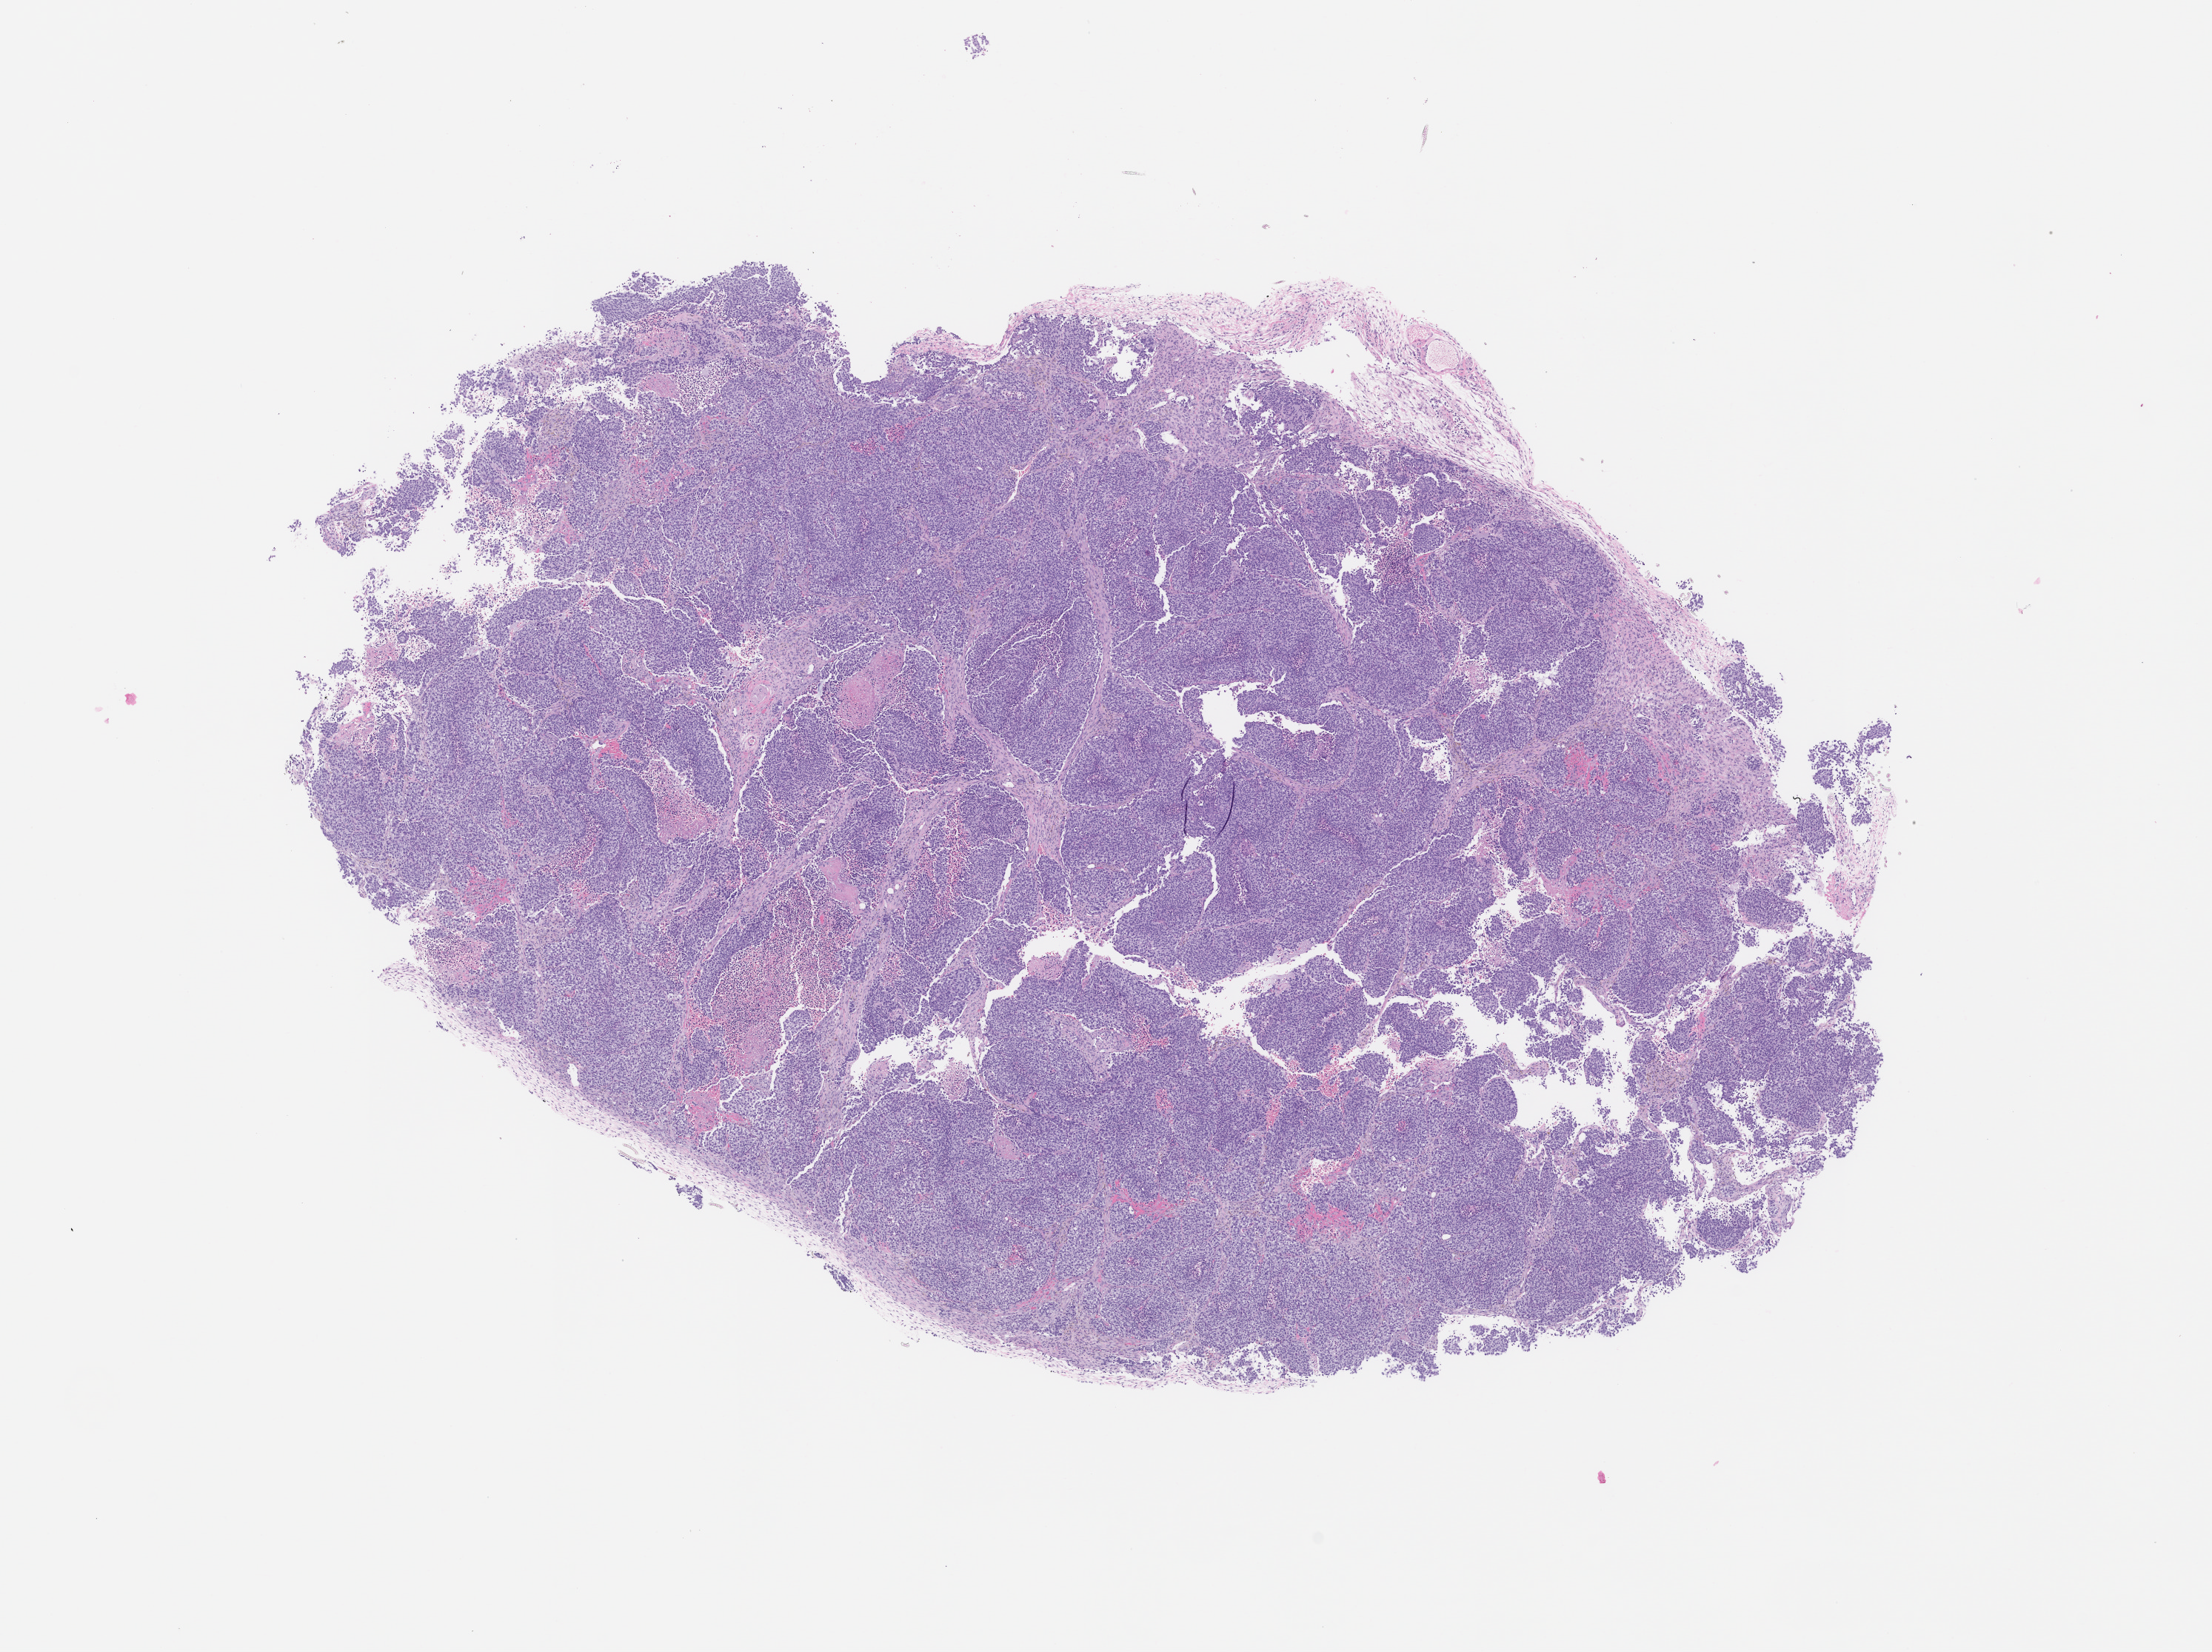
Whole-slide image, hematoxylin and eosin (H&E): patient-derived xenograft (human tumor grown in a mouse), shown as a low-resolution overview of the whole scanned area (about 12.0 x 8.9 mm); formalin-fixed, paraffin-embedded (FFPE) tissue; tumor site category: lung.
Originating patient diagnosis: Lung Adenocarcinoma.